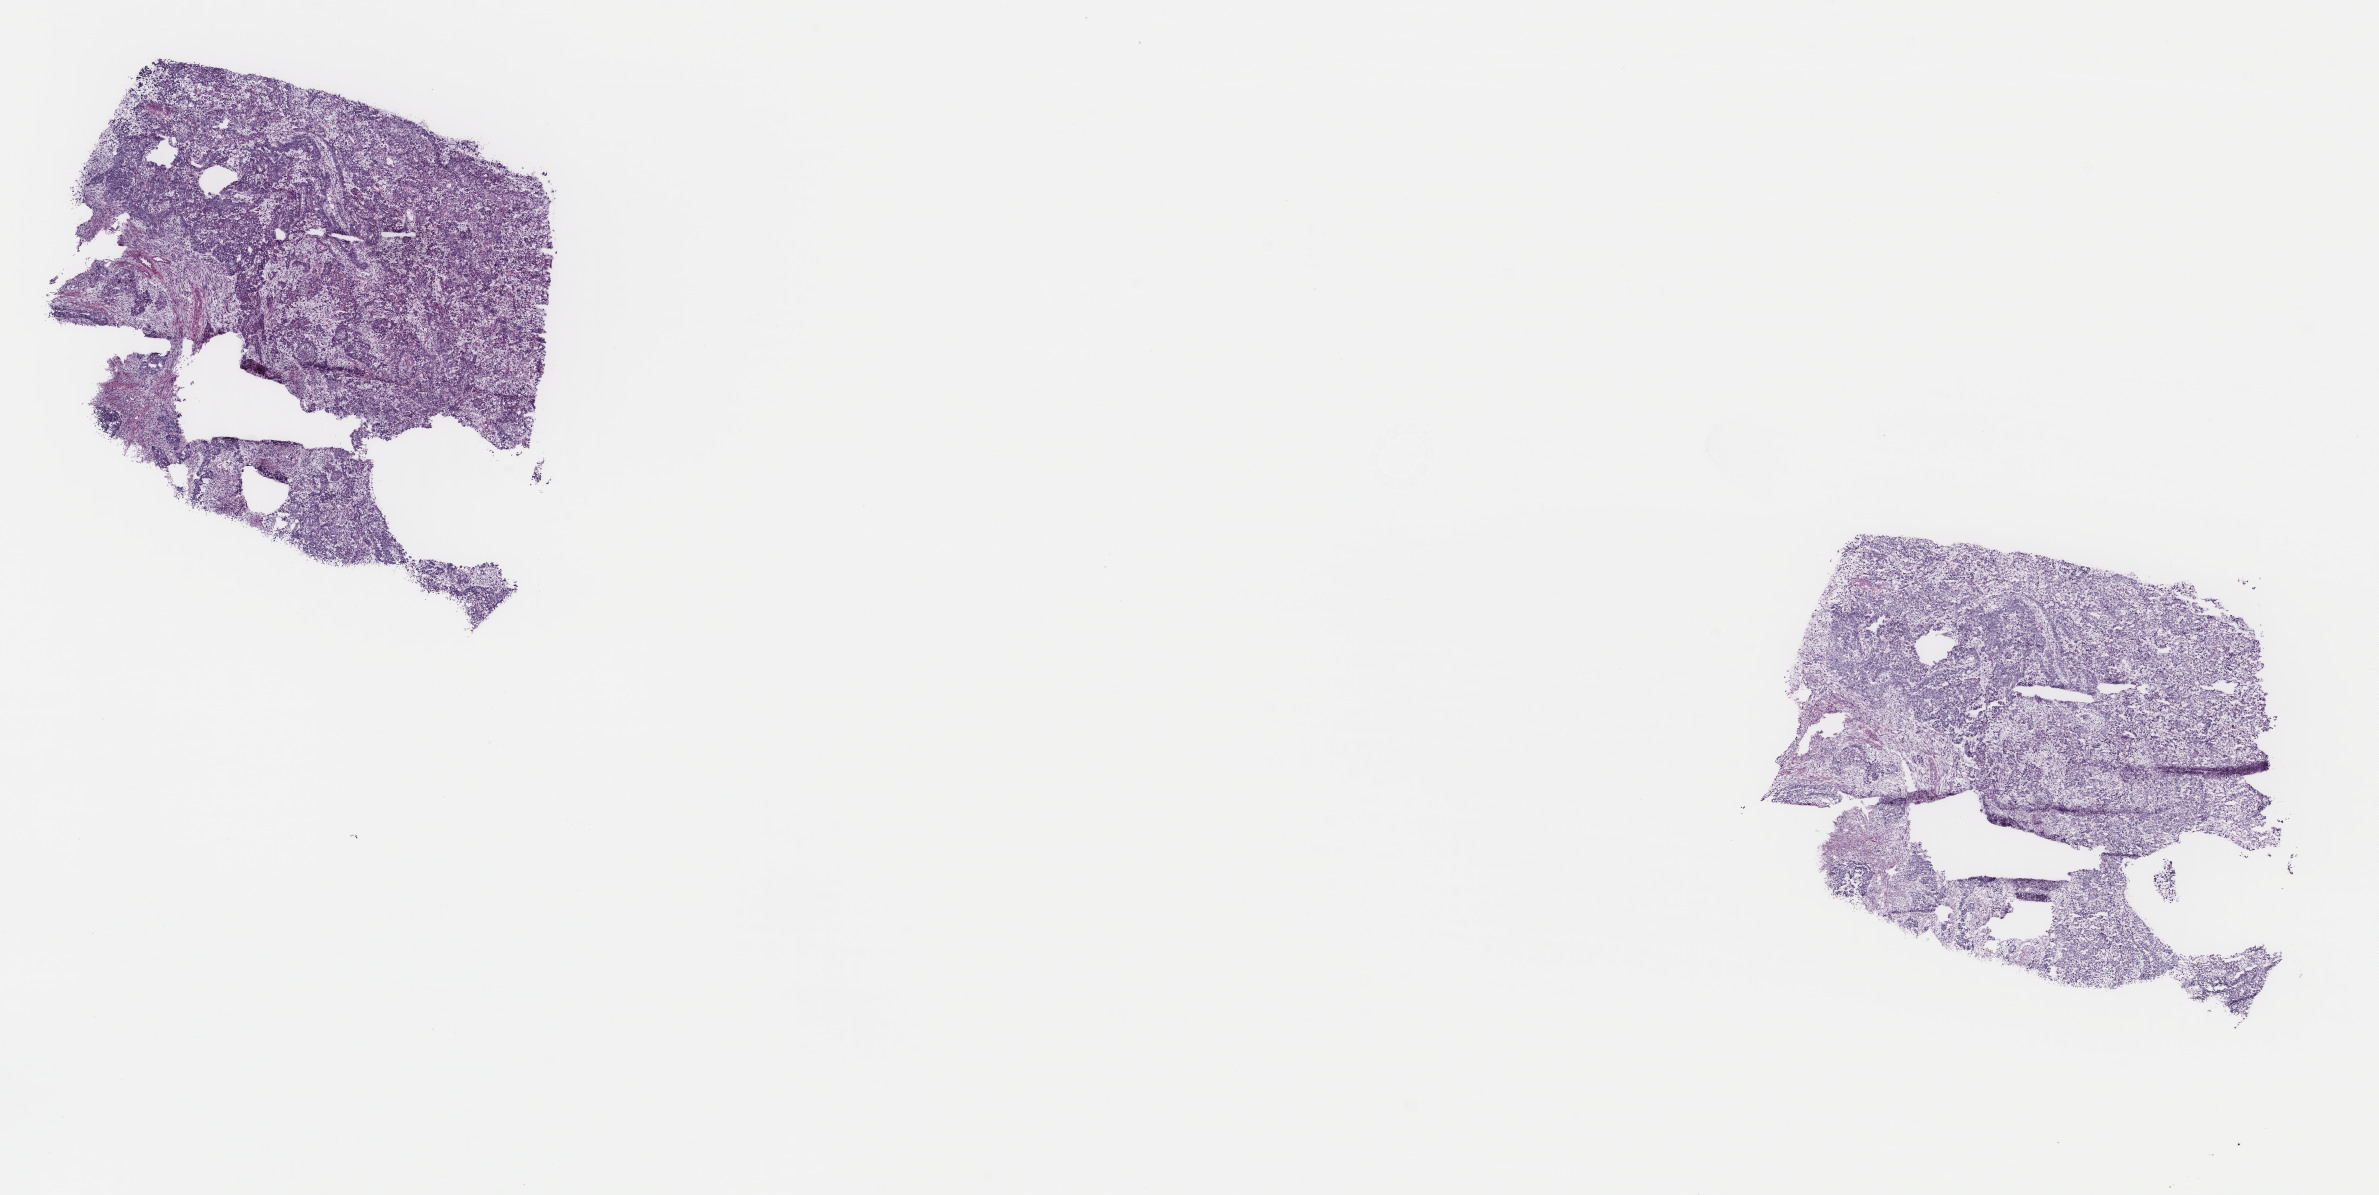
Digitized Hematoxylin and eosin (H&E) stained tissue section (whole slide), low-resolution overview of the scanned area, about 18.9 x 9.5 mm (acquisition: 40x scan). Frozen section from the top of the tissue portion. Sample: primary tumour, uterus. Female, age 71 years at initial diagnosis. Histologic grade: G3 (poorly differentiated). Composition of this section per pathologist review: tumour cells 70%, tumour nuclei 70%, normal cells 0%, stromal cells 25%, necrosis 5%. Inflammatory infiltration, as recorded: lymphocyte infiltration 40%, monocyte infiltration 20%, neutrophil infiltration 20%.
FIGO stage: IIIC1. Pathologic diagnosis: Serous cystadenocarcinoma, NOS (endometrium).